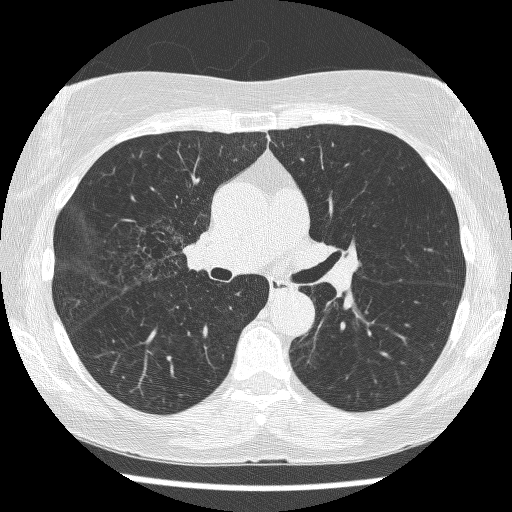
Low-dose screening chest CT, axial slice; baseline screening round; lung window (W 1500 / L -600 HU); 1.25 mm slice thickness; lung (sharp) reconstruction kernel (BONE). Female, age 64 years at enrolment.
Lesion marked by an expert reader, bounding box [x1, y1, x2, y2] px = [122, 214, 198, 274]. The screening reader recorded 3 non-calcified nodules or masses ≥4 mm on this exam (right upper lobe, right upper lobe, left lower lobe); which of them this box marks is not recorded. Official screen result: positive, change unspecified: nodule(s) >= 4 mm or enlarging nodule(s), mass(es), or other non-specific abnormalities suspicious for lung cancer. Lung cancer was diagnosed 735 days after this screen: adenocarcinoma, NOS, right upper lobe, right middle lobe, right hilum, stage IV (AJCC 6th edition), 85 mm at pathology.